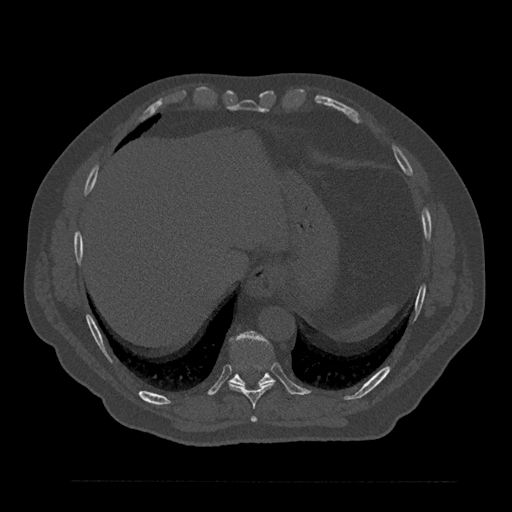
CT including the spine, one axial slice; slice 384 of 797 in the series (ordered by position); 120 kVp; bone window (W 1800 / L 400 HU); 0.5 mm slice thickness; 512 × 512 image matrix. Patient: male, 61 years. Case-level facts recorded for this patient, not image findings: primary cancer: prostate.
Outlined on this slice (semi-automatic segmentation, software-assisted and operator-edited):
- T10 vertebra: bounding box [x1, y1, x2, y2] px = [228, 332, 274, 386]
- T8 vertebra: [251, 417, 257, 422]
- T9 vertebra: [229, 366, 274, 409]